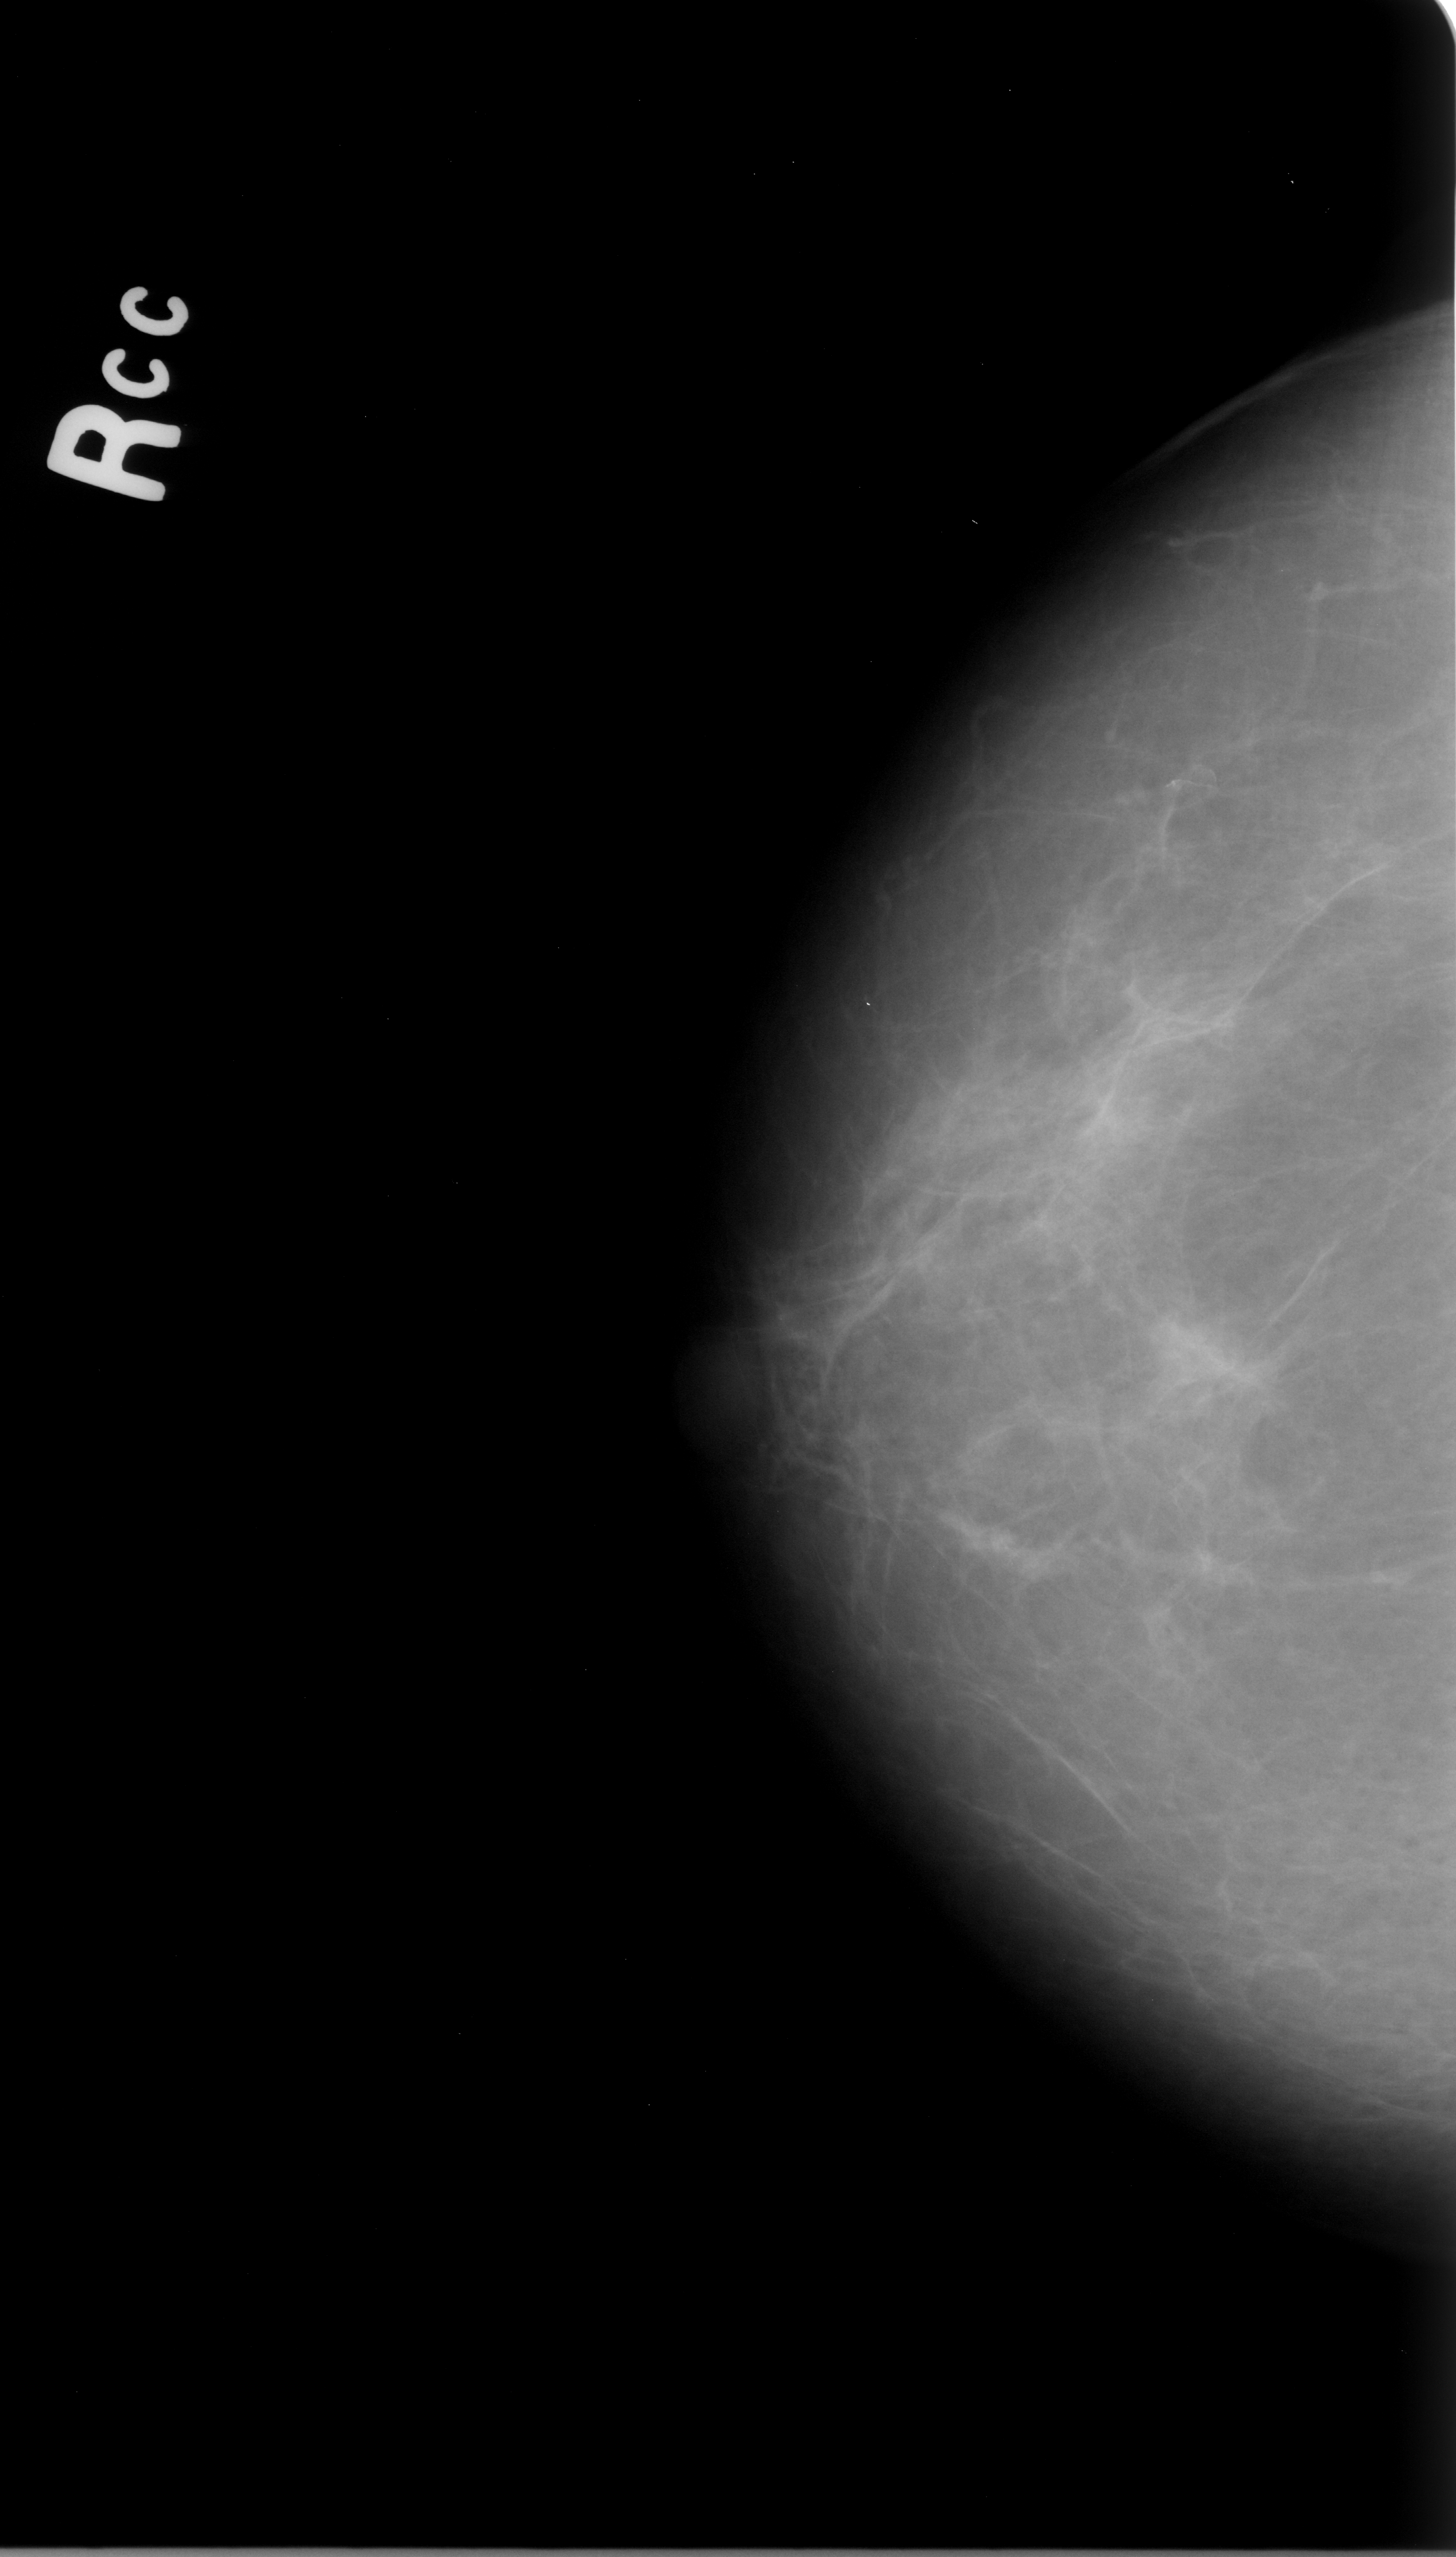
Mammogram (digitized film); right breast; CC view; 1456 × 2557 image matrix.
Expert-marked regions of interest on this image (one box per marked abnormality):
- mass, shape irregular, margins ill defined; BI-RADS assessment category 5; pathology result (as recorded, not read from the image): malignant: bounding box [x1, y1, x2, y2] px = [1134, 1299, 1293, 1472]